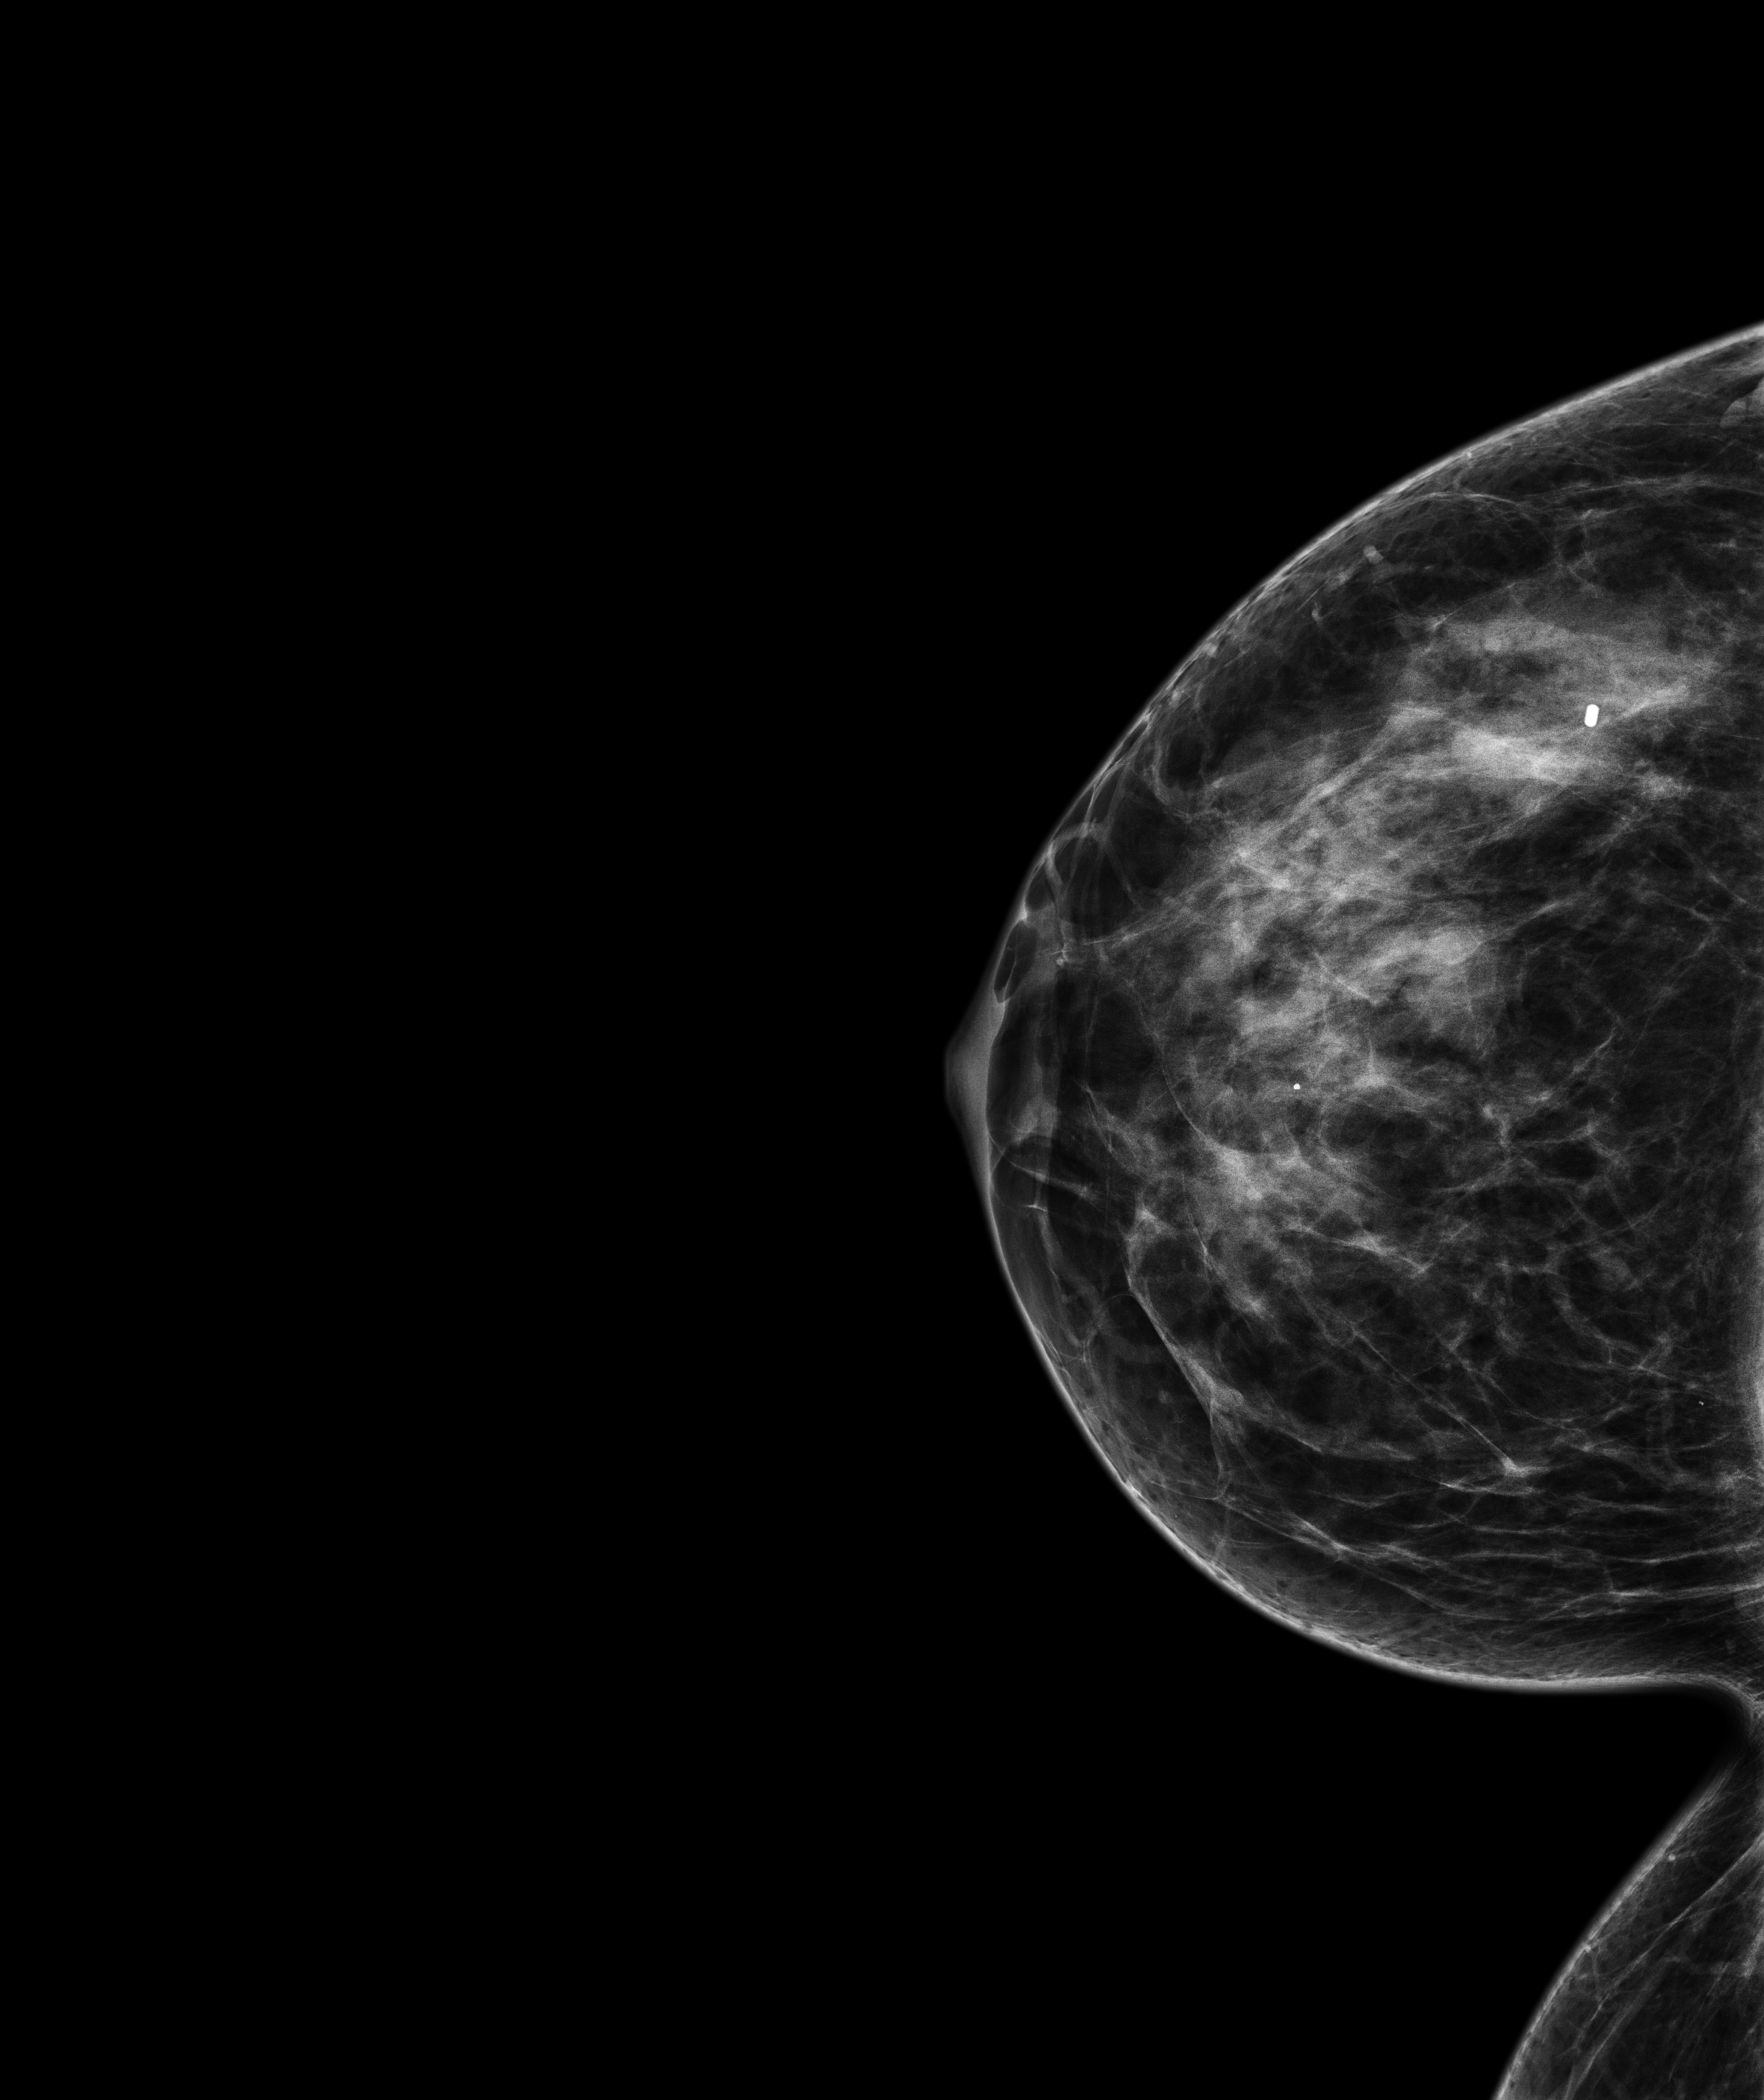
Annual screening mammography examination, system: Senographe Pristina. Patient aged 52 years (female).
Image type: full-field digital mammogram. Breast: right. Projection: craniocaudal (CC) view.